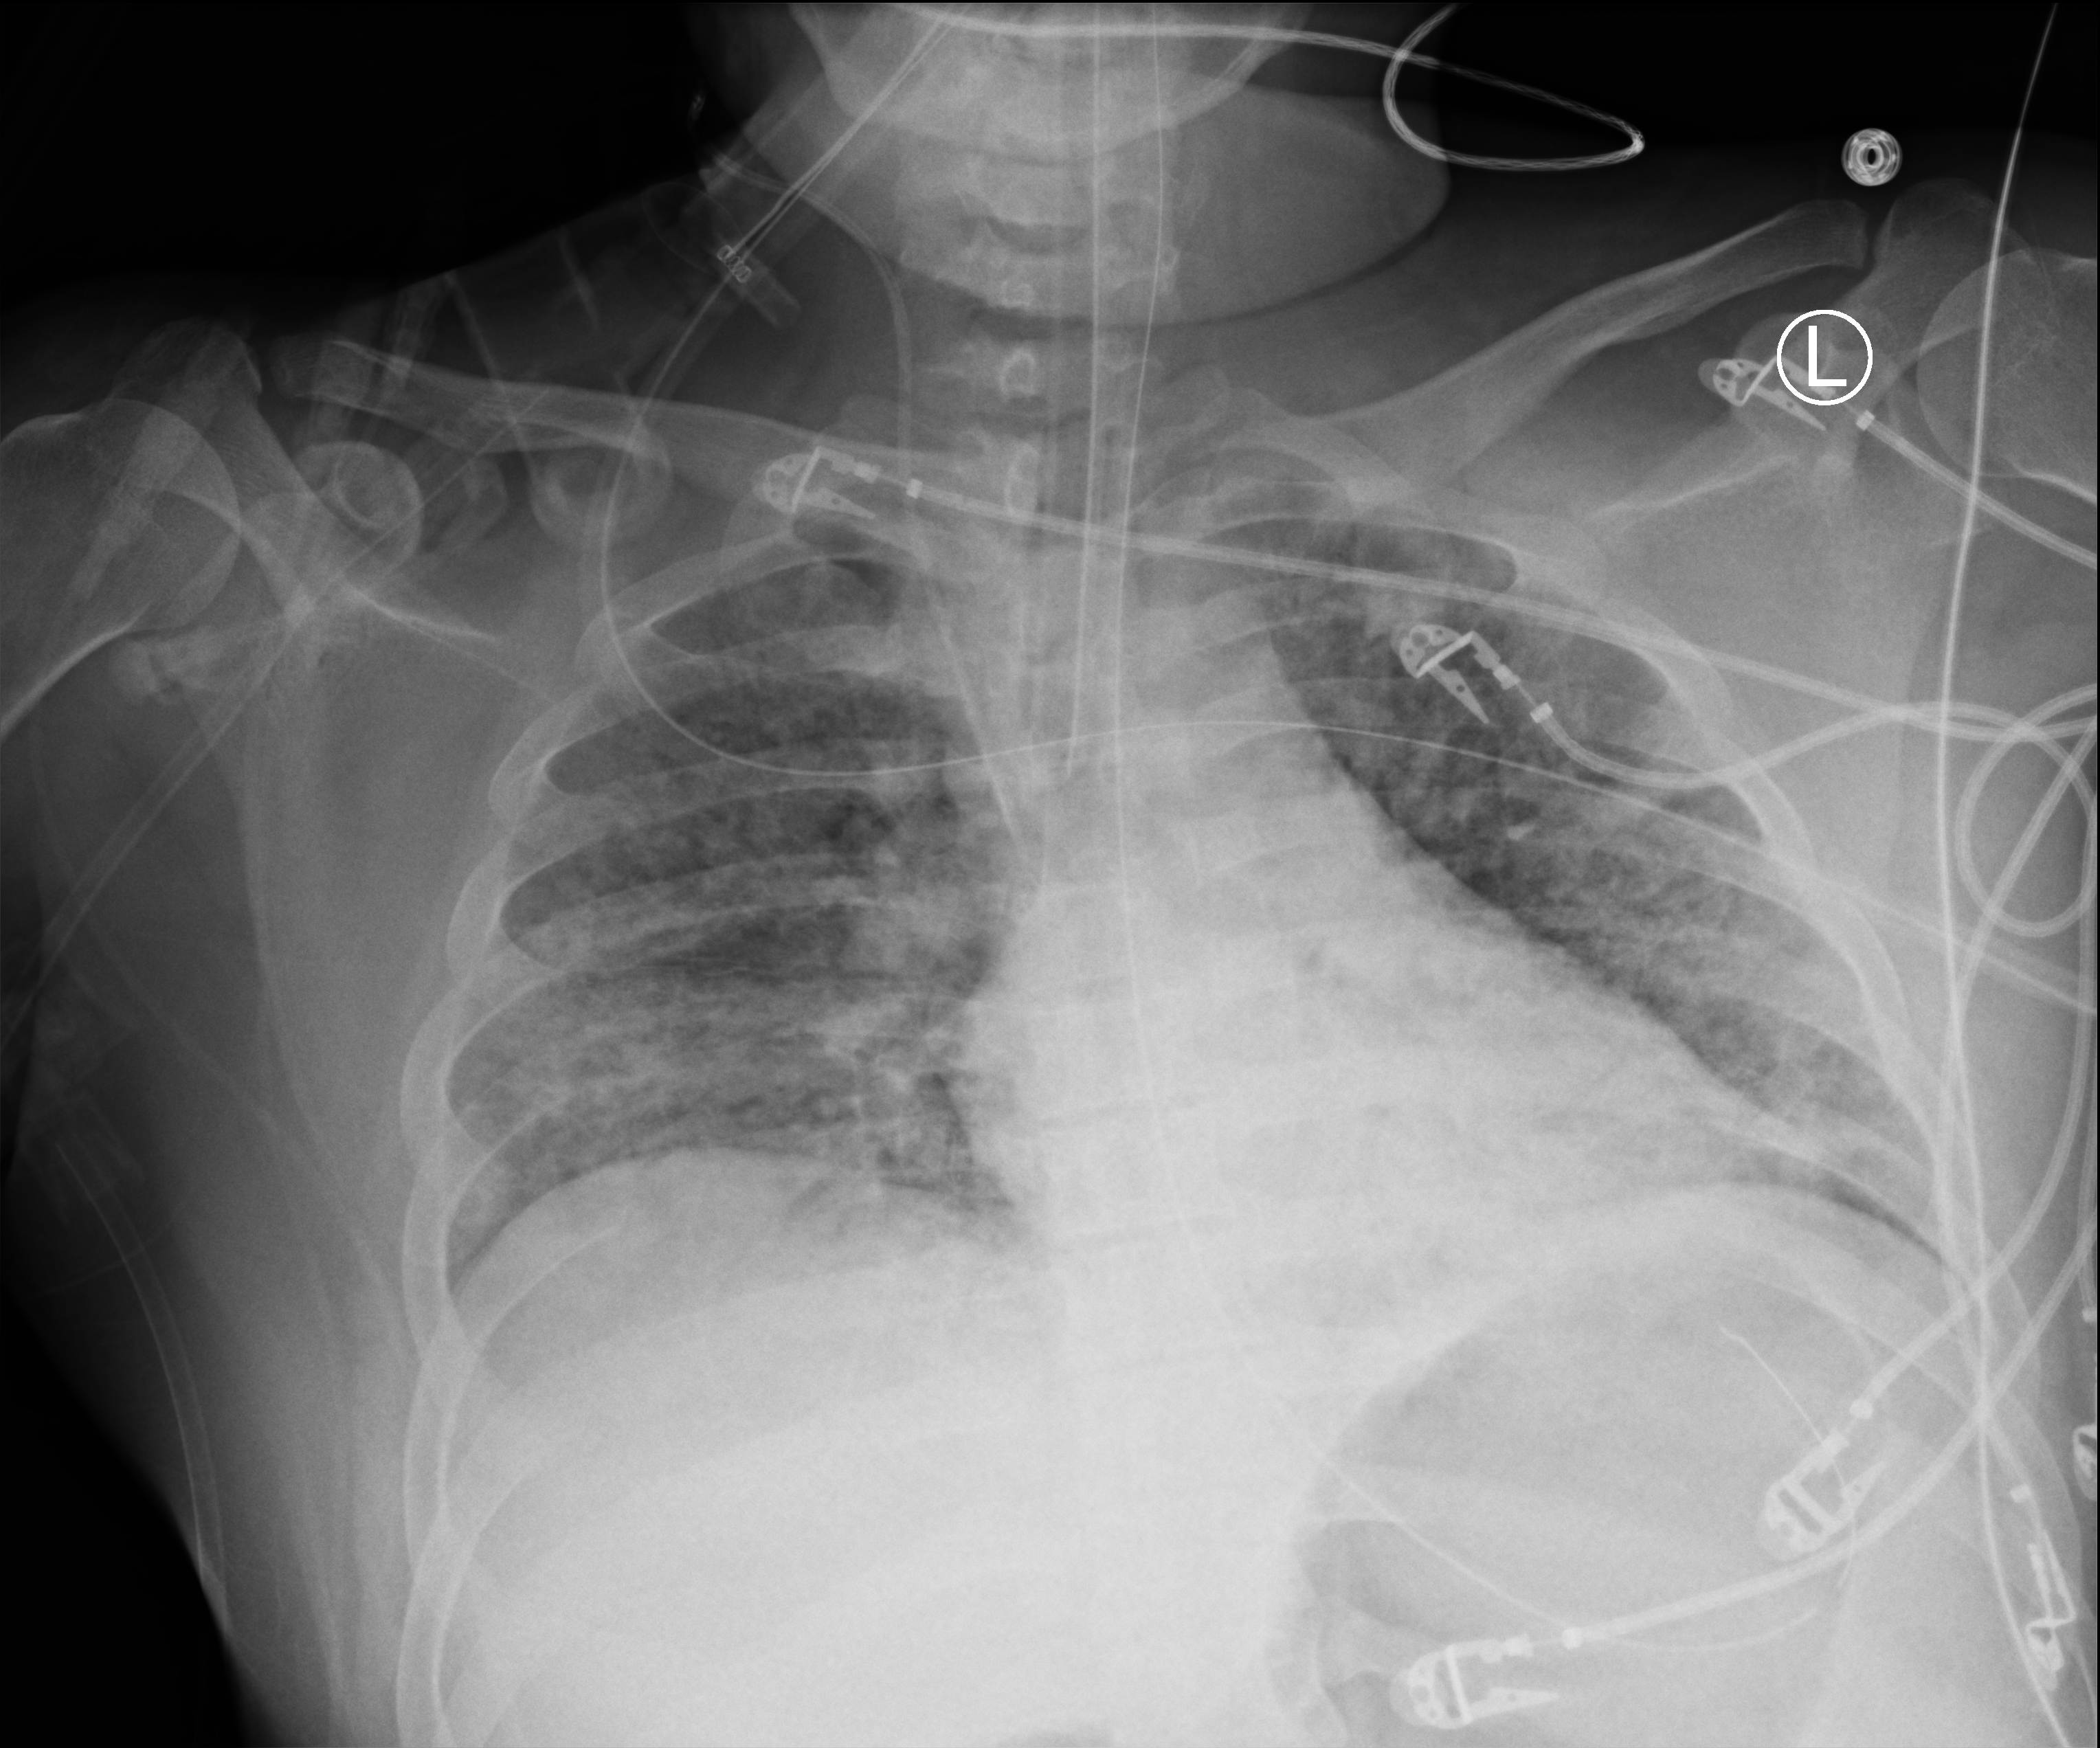
Chest X-ray (portable); anteroposterior (AP) projection. Patient hospitalised with COVID-19; male, aged 18–59 years.
From the hospital-stay record, not from the radiograph (when in the stay this image was taken is not recorded):
- other chronic lung disease (admission record): no
- length of hospital stay: 44 days
- COPD (admission record): no